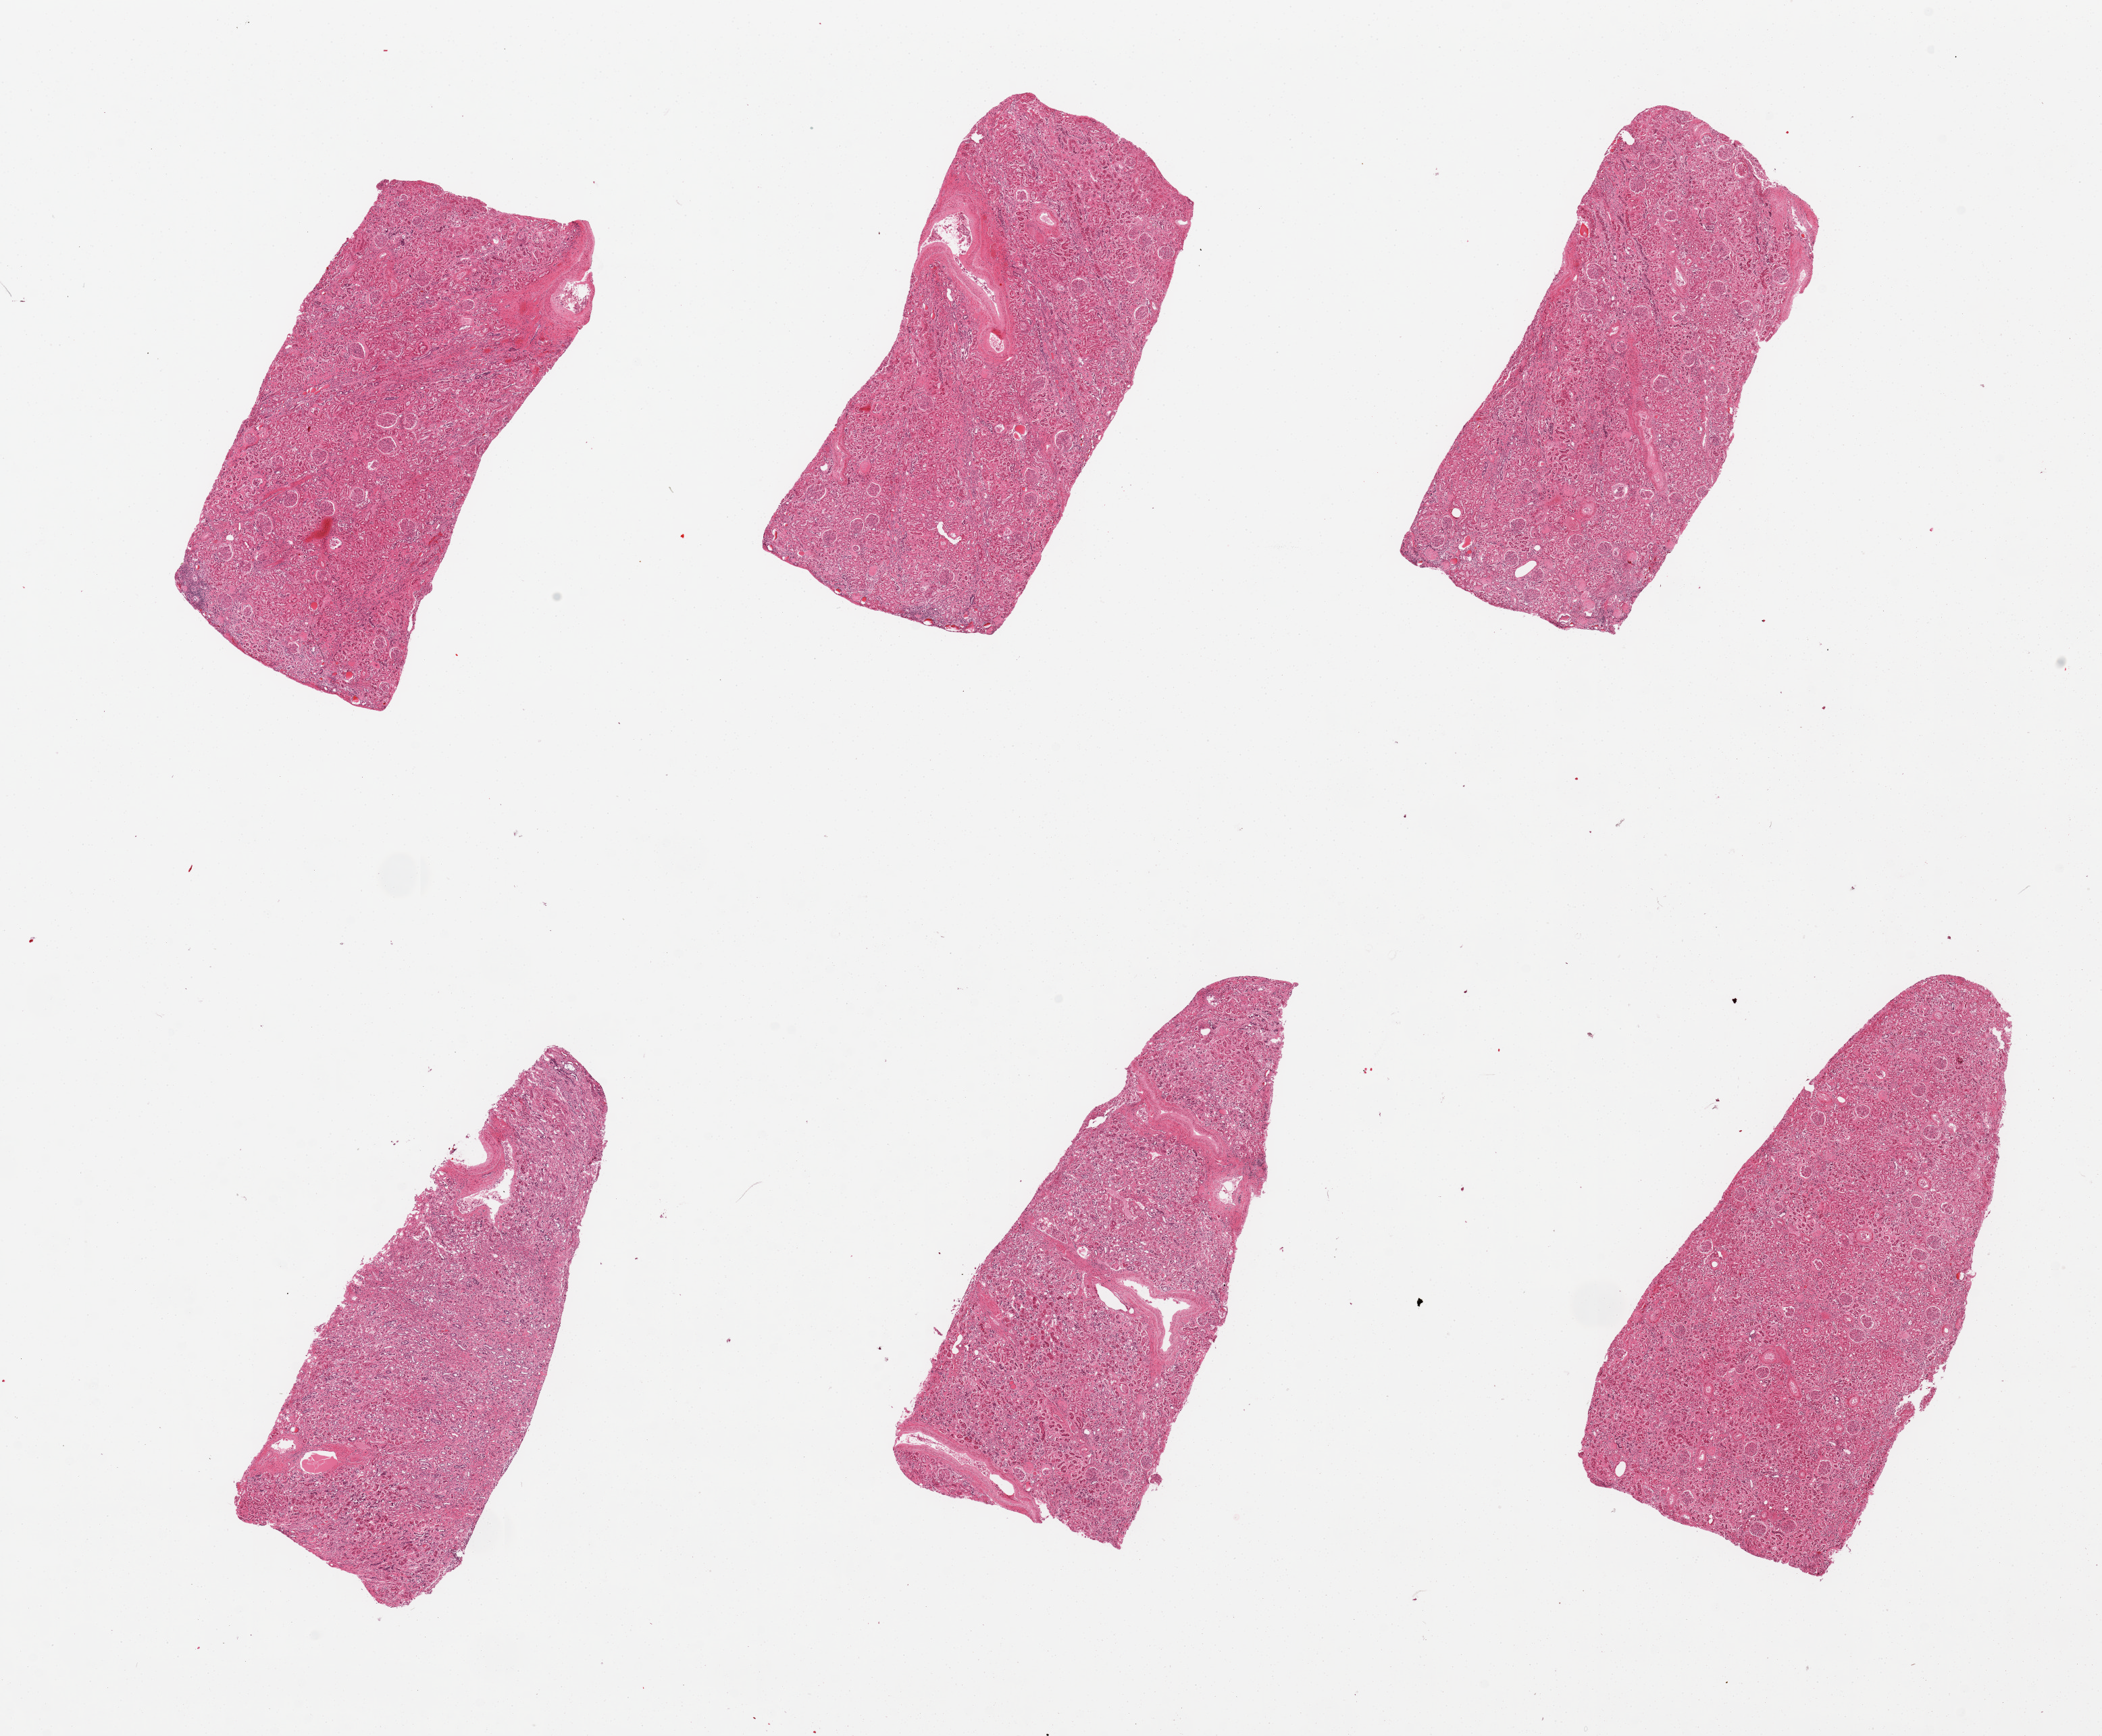
Digitized H&E-stained section, whole scanned area (about 24.6 x 20.3 mm, from a 20x scan) shown as a low-resolution overview. PAXgene-fixed paraffin-embedded (PFPE) section. Target tissue: renal cortex. Donor tissue sample. Donor sex: male.
Pathologist's review note for this sample: 6 pieces; glomeruli present, markedly autolyzed.